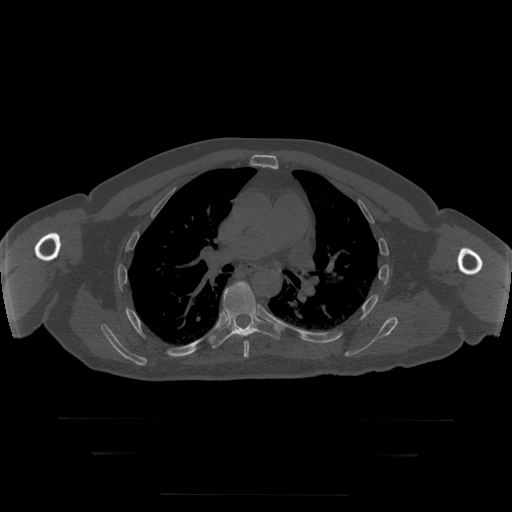
CT including the spine, one axial slice; slice 193 of 397 in the series (ordered by position); reconstruction kernel STANDARD; bone window (W 1800 / L 400 HU); 1.25 mm slice thickness; 512 × 512 image matrix, field of view 510 × 510 mm. Patient age 73 years. From the clinical record (not read from this slice): primary cancer: prostate.
Structures marked on this image (semi-automatic segmentation, software-assisted and operator-edited):
- T6 vertebra: bounding box <240,336,249,358> (left, top, right, bottom; pixels)
- T7 vertebra: <210,282,281,349>